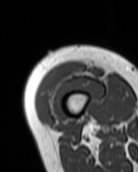
MRI of an extremity soft-tissue mass, one axial slice; slice 8 of 99 in the series (ordered by position); MR volume resampled by the dataset authors to the PET/CT grid (not the native acquisition matrix); 3.27 mm slice thickness; 138 × 172 image matrix, field of view 135 × 168 mm. Female patient. Case-level facts recorded for this patient, not image findings: histological type: pleiomorphic undifferentiated sarcoma; grade: high; site of the primary tumour: right quadricep.
Outlined on this slice (expert contour drawn on MRI and transferred to this co-registered scan by the dataset authors):
- gross tumour volume including surrounding oedema: bounding box (x1, y1, x2, y2) in pixels: (58, 61, 84, 74)